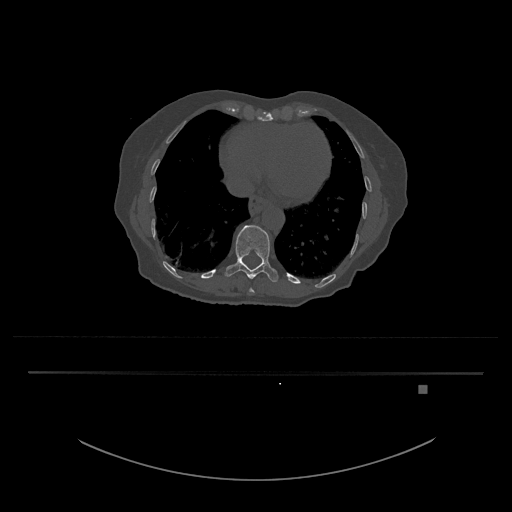
CT including the spine, one axial slice. Position 670 of 797 along the scan axis. Reconstruction kernel Br40s/3. 120 kVp. Bone window (W 1800 / L 400 HU). 0.5 mm slice thickness. 512 × 512 image matrix, field of view 500 × 500 mm. Patient: female, 57 years. From the clinical record (not read from this slice): primary cancer: cervical.
Annotated regions visible in this slice (semi-automatic segmentation, software-assisted and operator-edited):
- T10 vertebra: box from (x=249, y=288) to (x=255, y=293) px
- T11 vertebra: (x=225, y=225)–(x=279, y=282)